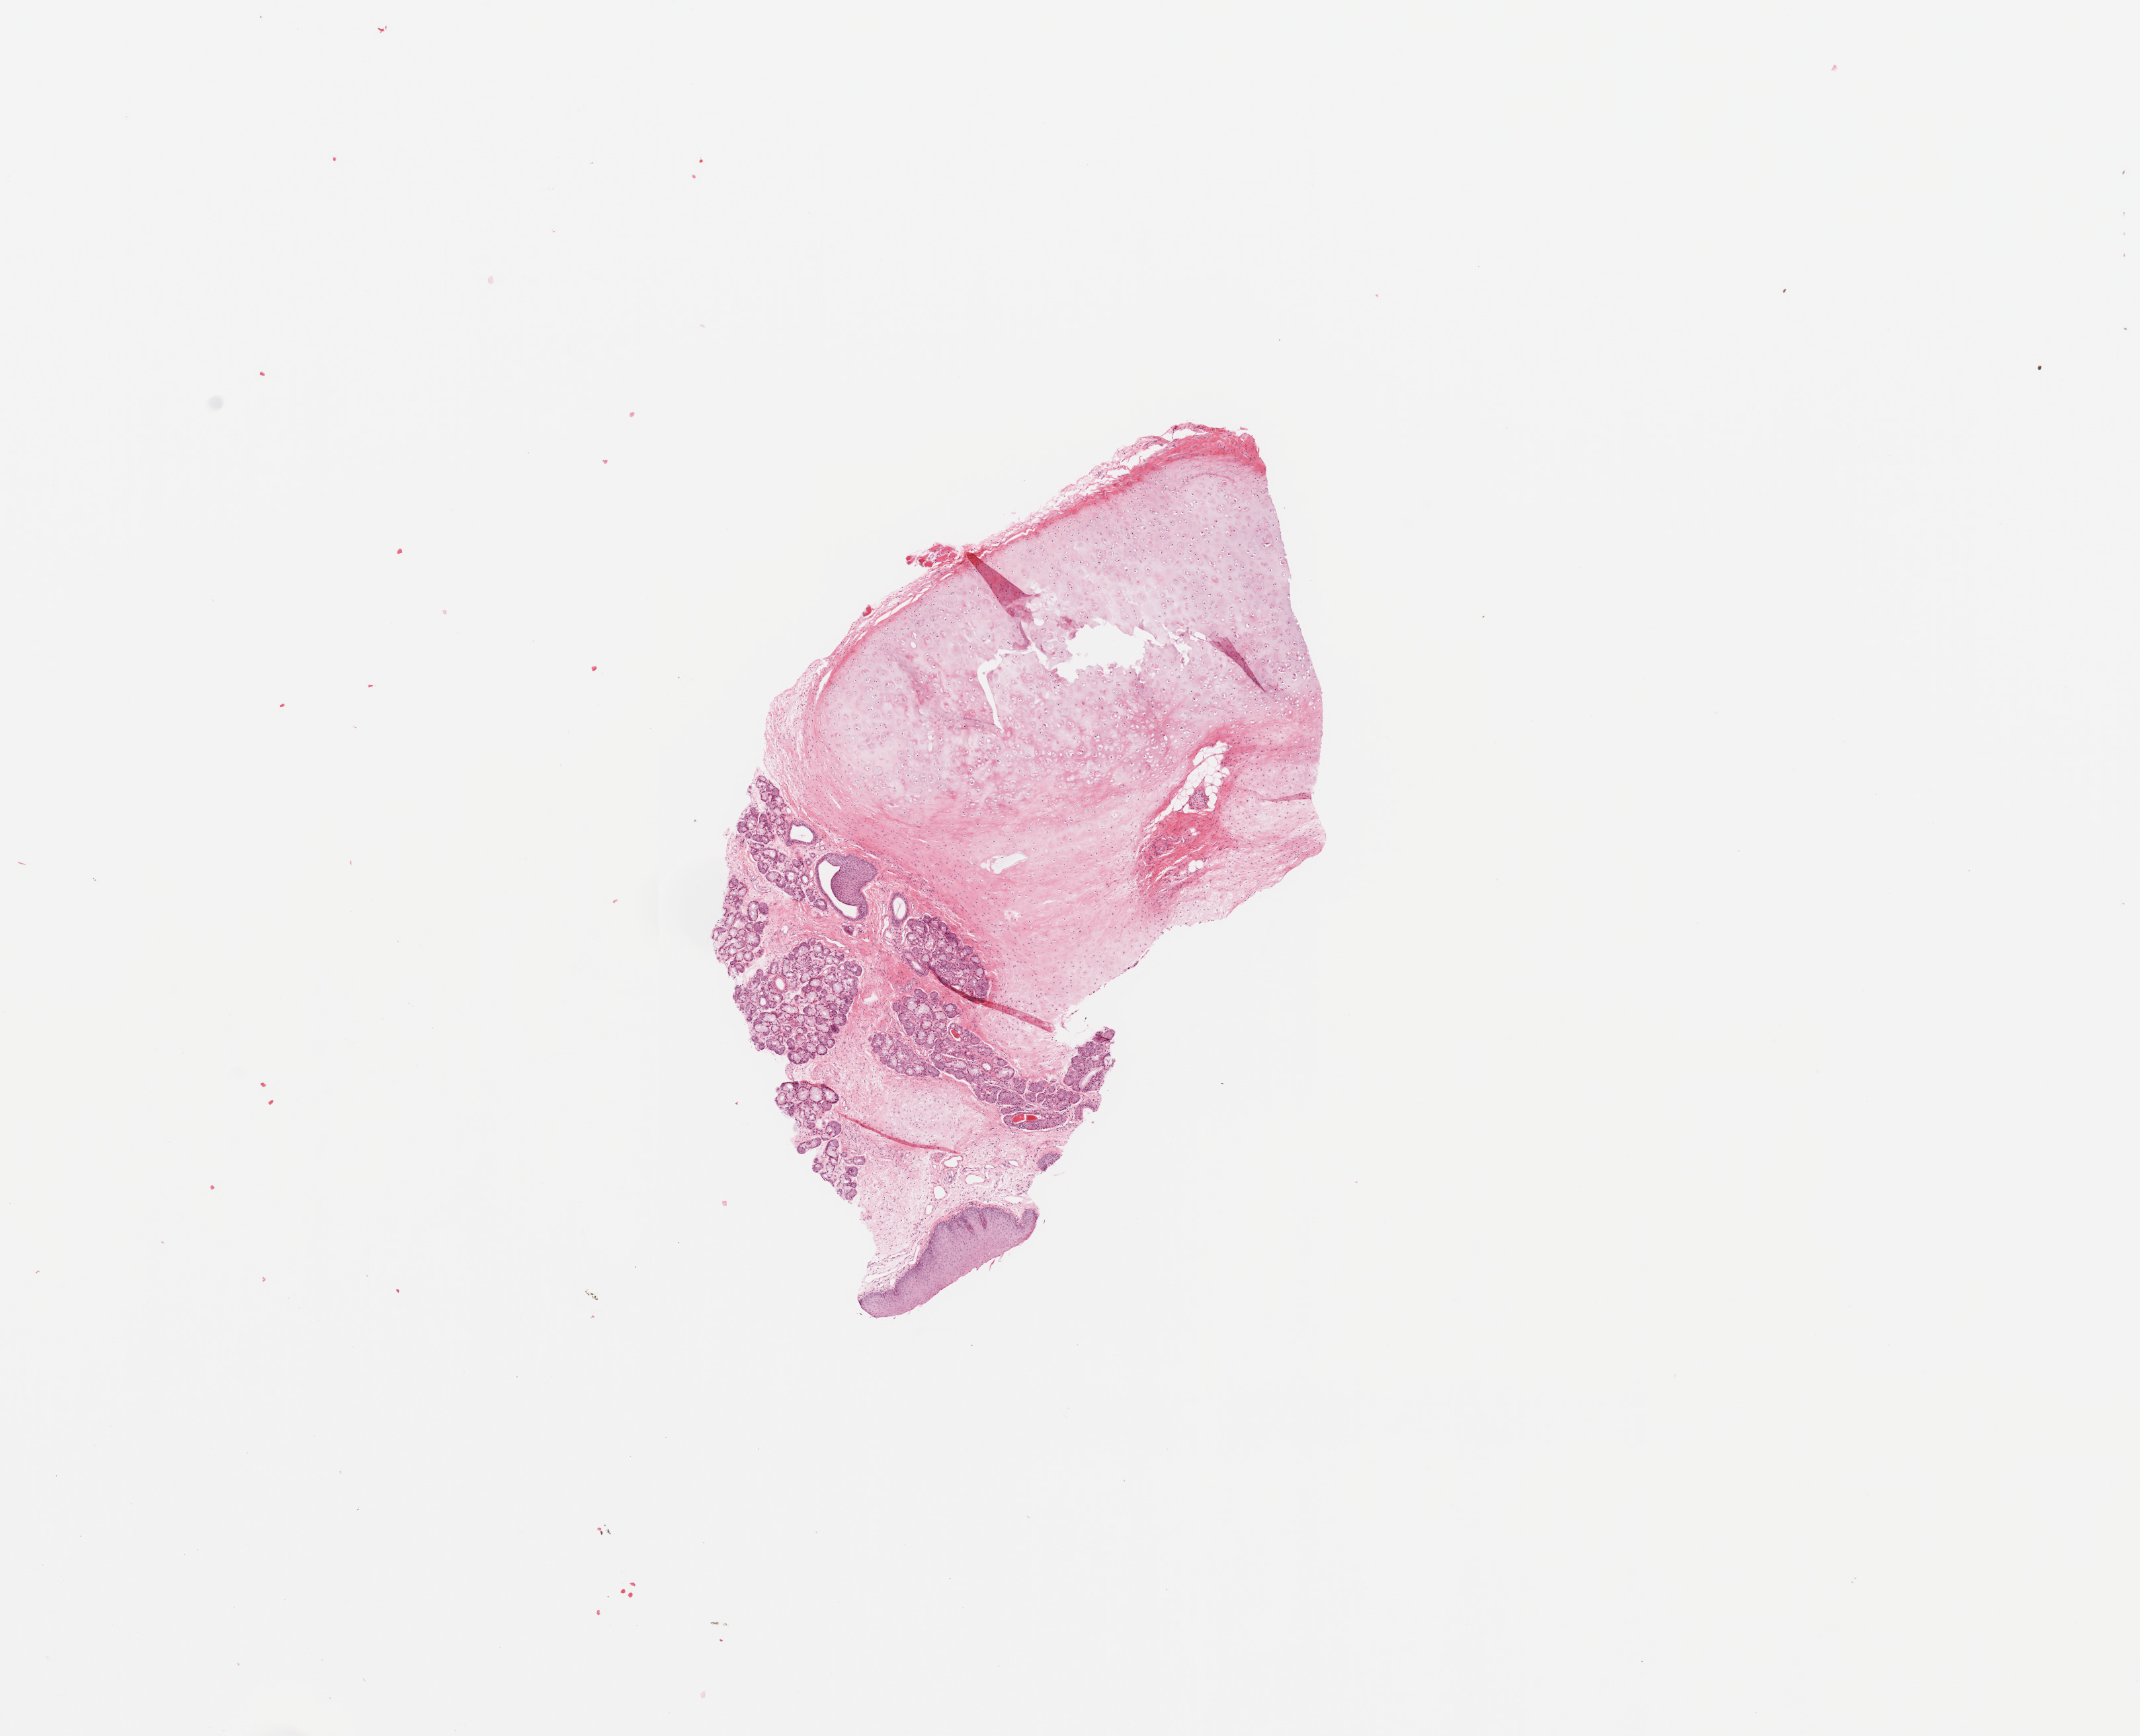
Digitized Hematoxylin and eosin (H&E) stained tissue section (whole slide), whole scanned area (about 12.8 x 10.4 mm, from a 20x scan) shown as a low-resolution overview. Normal (non-tumour) tissue sample, sampled site: larynx. Patient: female, age 63 years.
- this section: normal (non-tumour) tissue from the same patient
- patient diagnosis: Squamous cell carcinoma, NOS